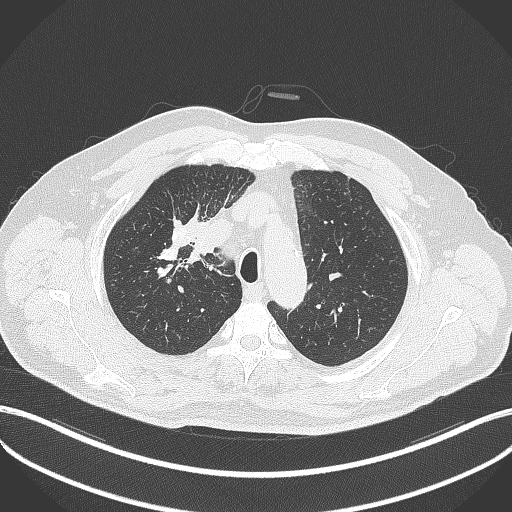
Chest CT, one axial slice; slice 306 of 411 in the series (ordered by position); 120 kVp; lung window (W 1500 / L -600 HU); 1 mm slice thickness; 512 × 512 image matrix, field of view 400 × 400 mm. Male patient, age 60 years. Case-level facts recorded for this patient, not image findings: clinical TNM (as recorded): T1b N1 M0.
Structures marked on this image (bounding box drawn by a radiologist):
- lung tumour (recorded histology: squamous cell carcinoma): bounding box [x1, y1, x2, y2] px = [187, 231, 217, 262]